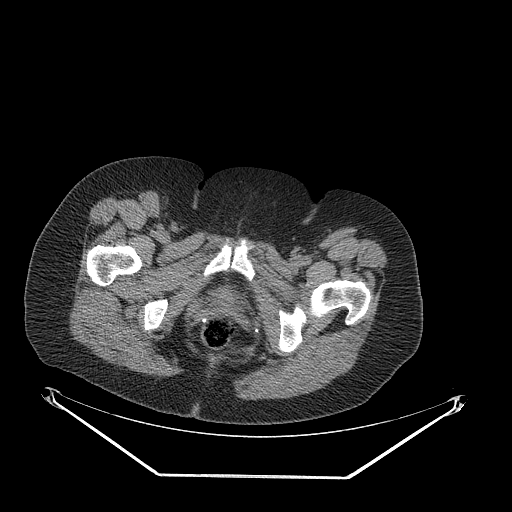
CT of an extremity soft-tissue mass (from a PET/CT study), one axial slice. Slice 62 of 257 in the series (ordered by position). 140 kVp. Soft-tissue window (W 400 / L 40 HU). 512 × 512 image matrix, field of view 500 × 500 mm. Female patient. From the clinical record (not read from this slice): histological type: synovial sarcoma; grade: intermediate; site of the primary tumour: right buttock.
Outlined on this slice (expert contour drawn on MRI and transferred to this co-registered scan by the dataset authors):
- gross tumour volume including surrounding oedema: bounding box [x1, y1, x2, y2] px = [103, 317, 134, 337]